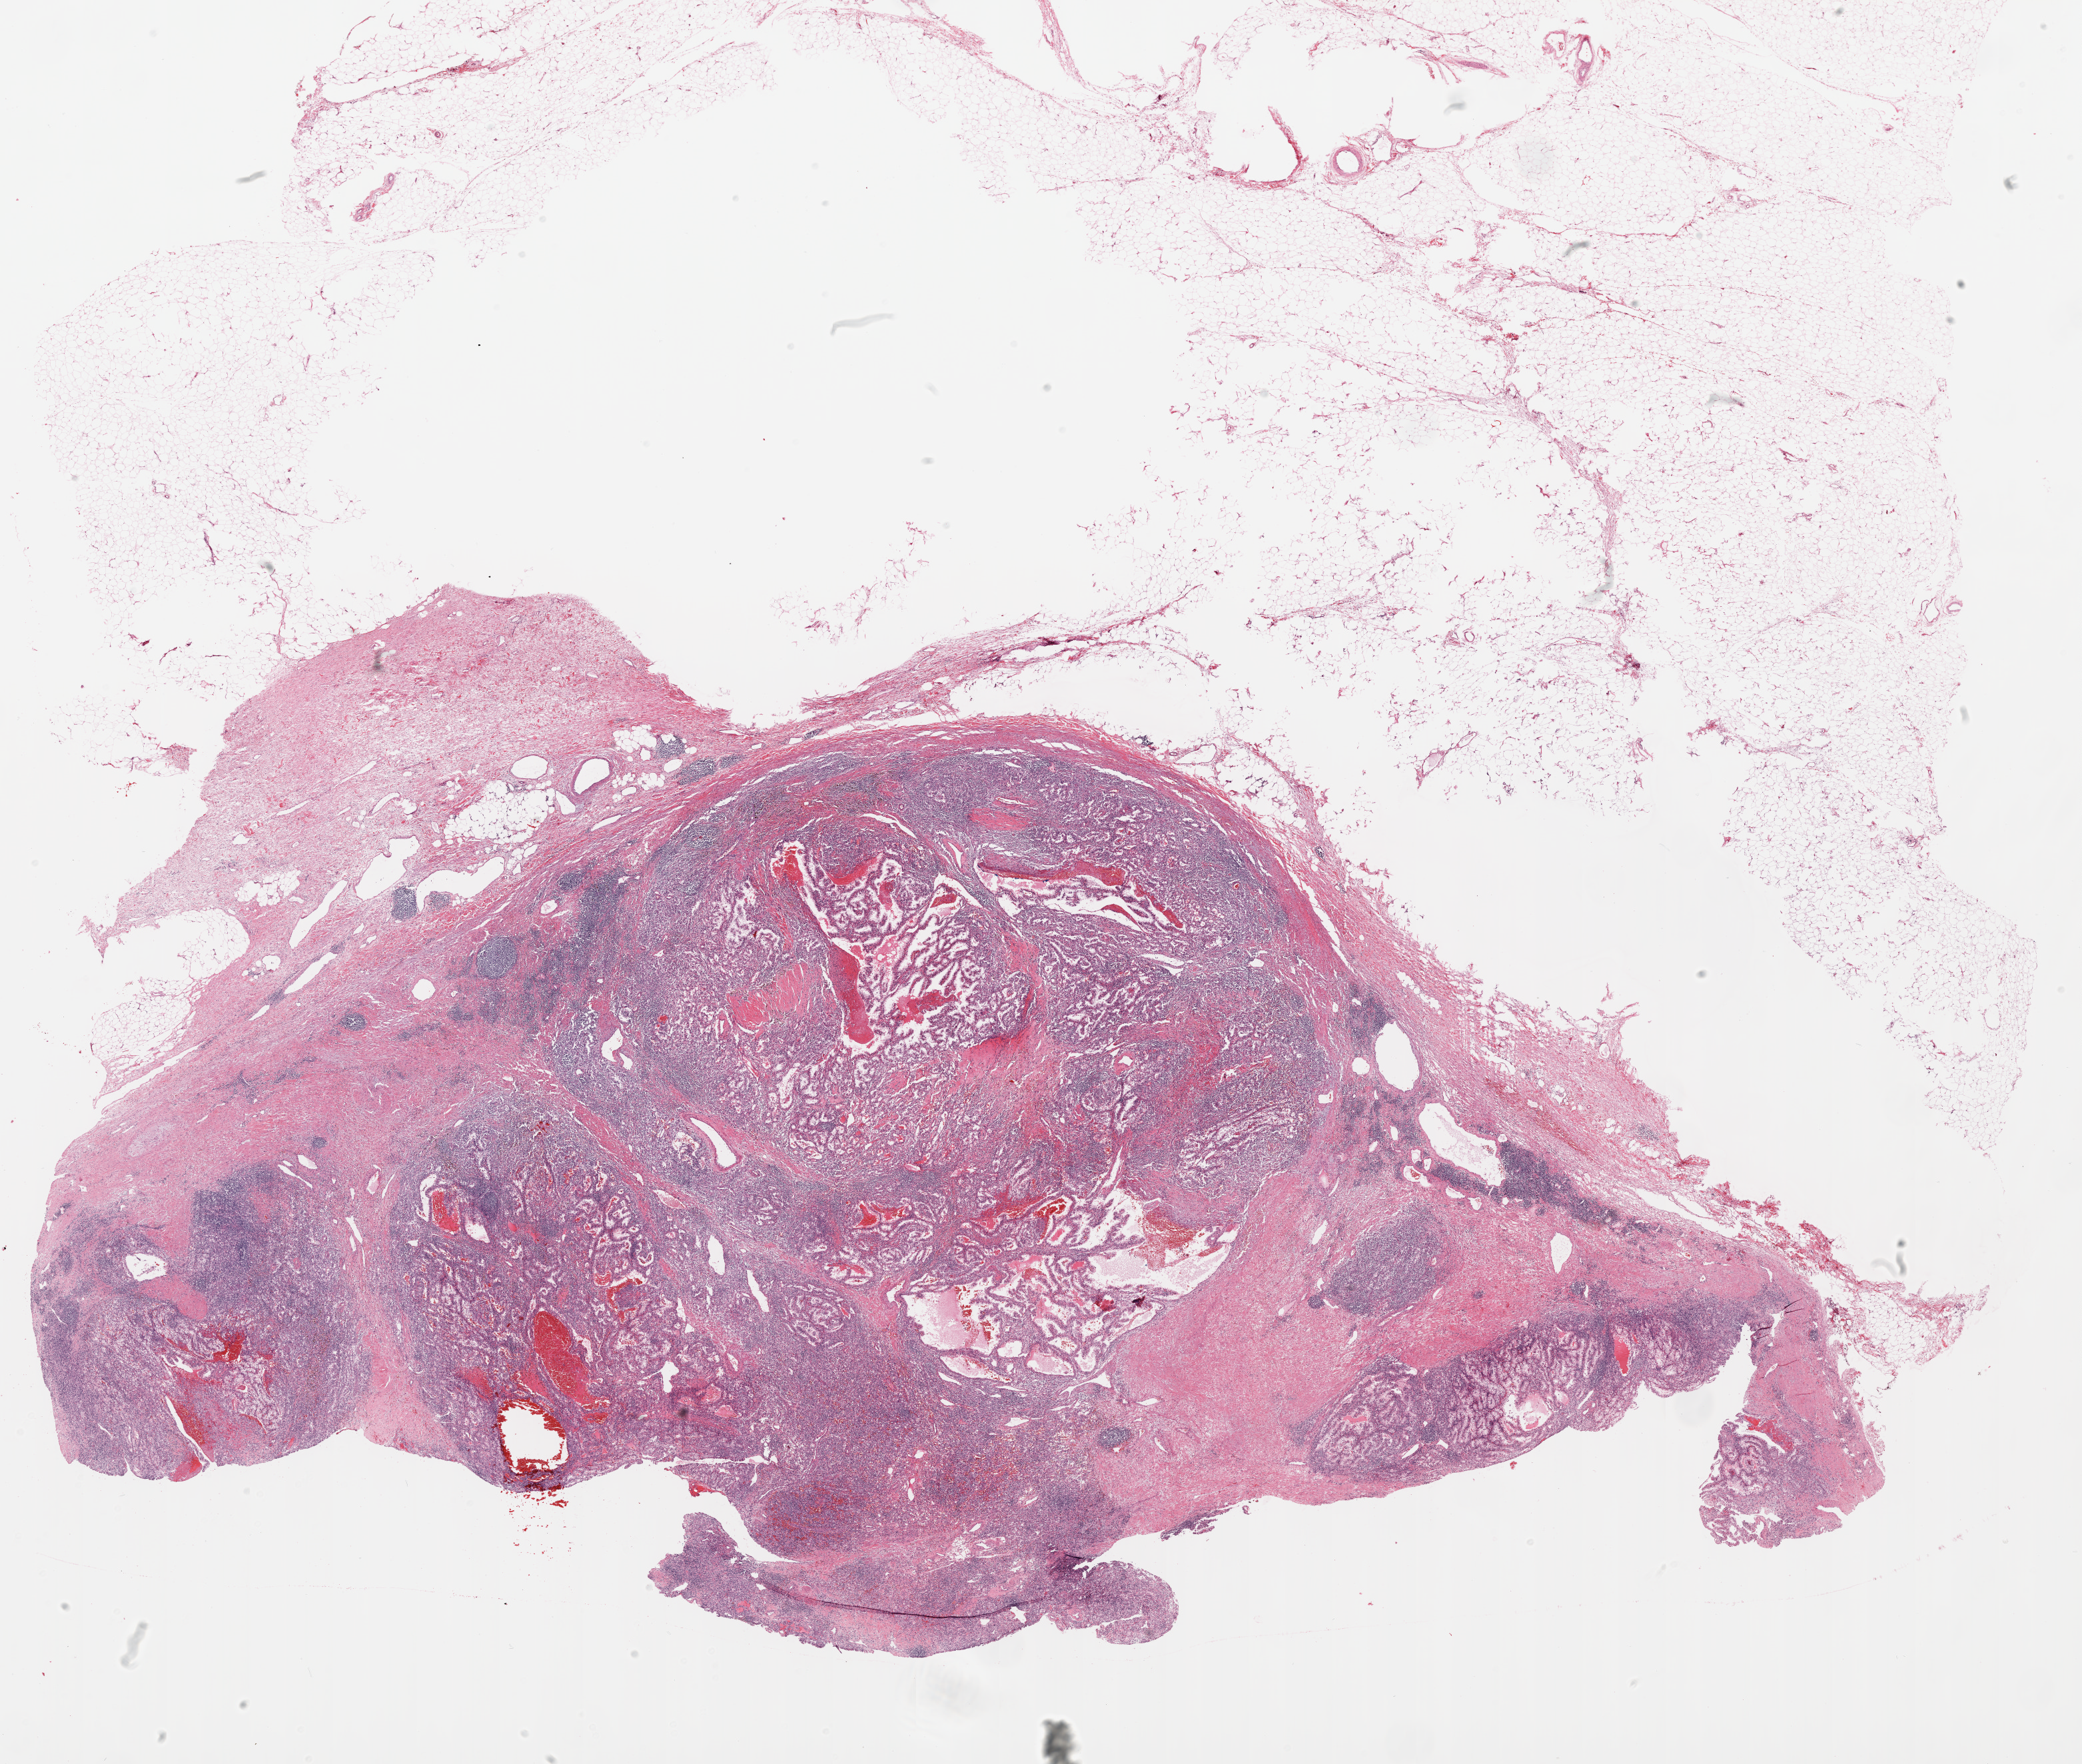
Digitized H&E-stained tissue section (whole slide) — whole scanned area (about 25.1 x 21.2 mm, slide scanned at 20x) shown as a low-resolution overview; formalin-fixed paraffin-embedded (FFPE) diagnostic section; sample: primary tumour, kidney. Male, age 46 years at initial diagnosis.
Diagnosis: Clear cell adenocarcinoma, NOS.